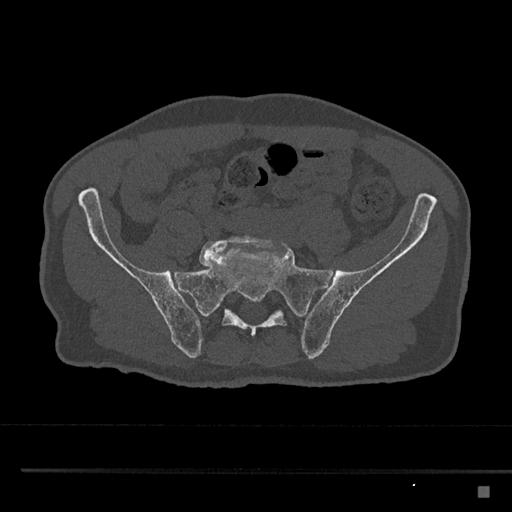
CT including the spine, one axial slice. Reconstruction kernel Br40s/3. Bone window (W 1800 / L 400 HU). 0.5 mm slice thickness. 512 × 512 image matrix. Male patient, age 59 years. From the clinical record (not read from this slice): primary cancer: prostate.
Annotated regions visible in this slice (semi-automatically segmented with operator editing):
- L5 vertebra: box from (x=199, y=235) to (x=285, y=268) px